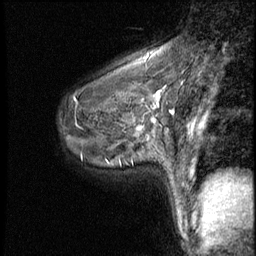
Breast MRI (dynamic contrast-enhanced), one sagittal slice; slice 38 of 50 in the series (ordered by position); 3 images stored at this slice position (order not interpretable as contrast timing); 1.5 T; TE 4.2 ms, TR 8.7 ms; 2.5 mm slice thickness; 256 × 256 image matrix. Patient: female, 43 years. From the clinical record (not read from this slice): setting: breast cancer imaged before/during neoadjuvant chemotherapy; receptor status: HR-positive, HER2-negative.
Structures marked on this image (semi-automatic segmentation, software-assisted and operator-edited):
- analysis volume of interest (the breast-tissue region the enhancement analysis was run in; not a lesion): bounding box <122,109,159,155> (left, top, right, bottom; pixels)
- tumour enhancement mask (voxels above the 140 % enhancement threshold inside the analysis volume of interest): <136,119,157,130>